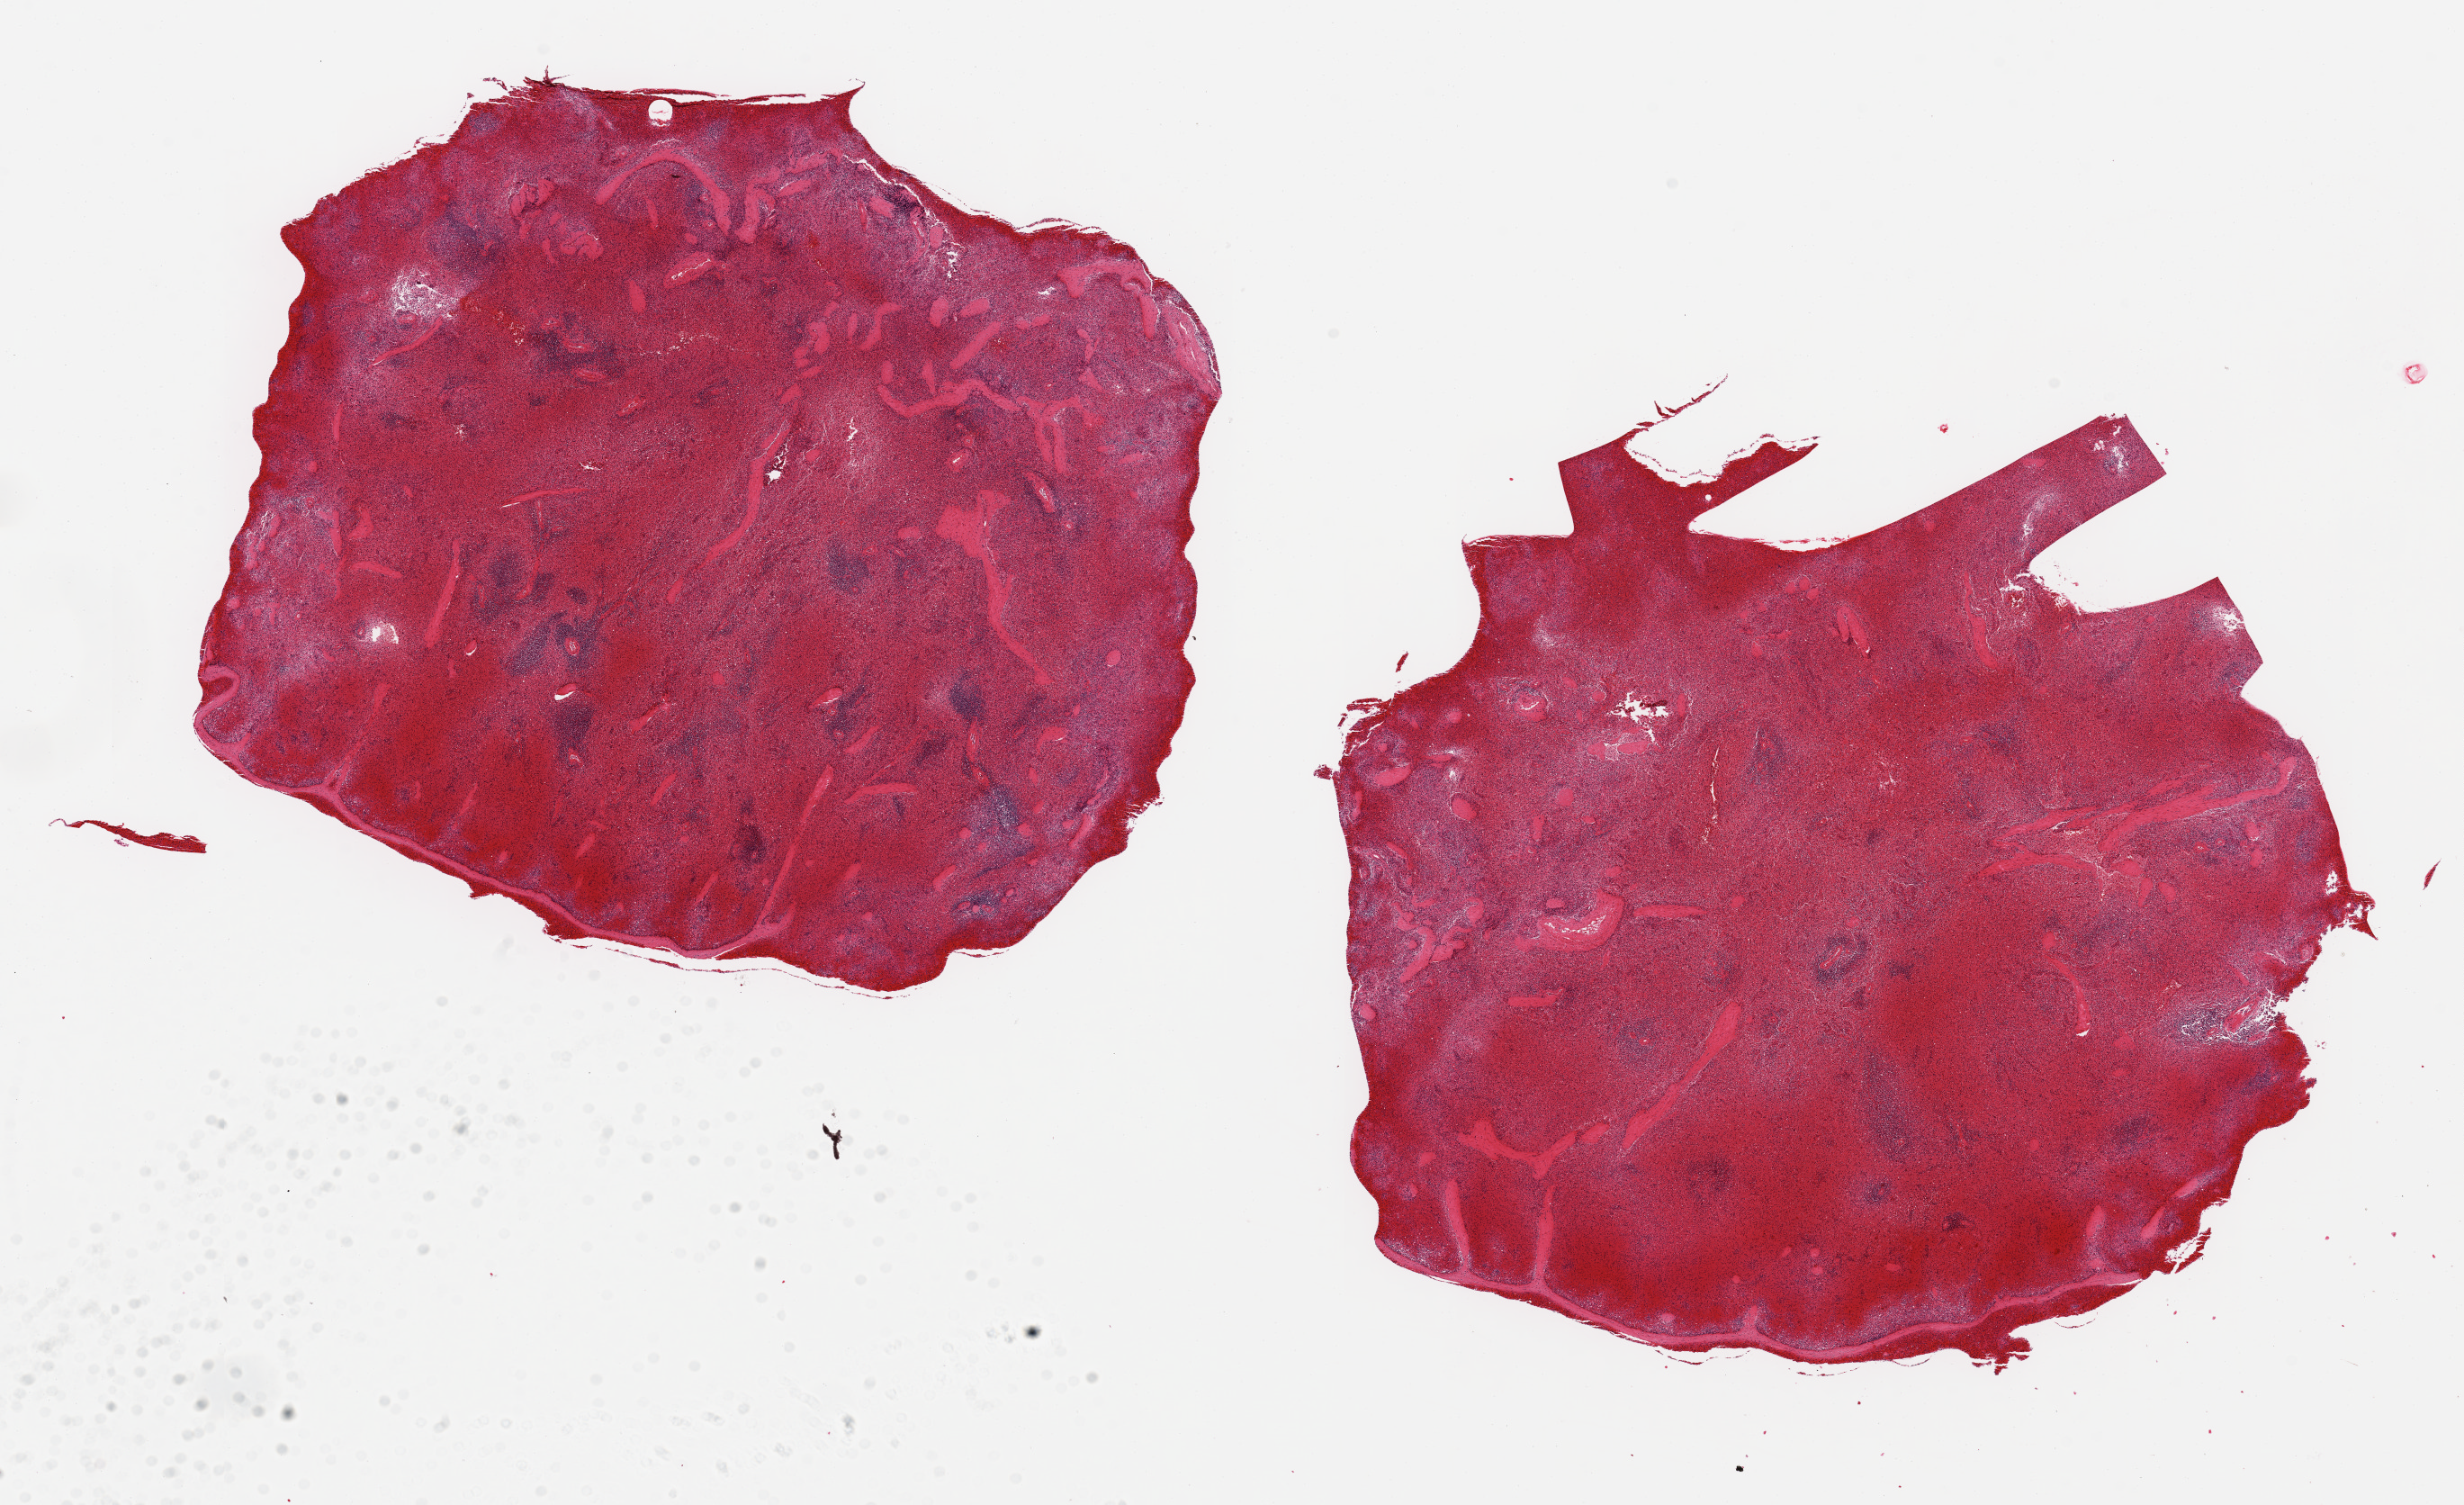
Digitized hematoxylin and eosin (H&E)-stained section, a low-resolution overview of the entire scanned area, about 21.7 x 13.2 mm (acquisition: 20x scan), PAXgene-fixed paraffin-embedded (PFPE) section, sampled site (target tissue): spleen, donor tissue sample. Female donor.
• review note (as recorded): 2 8x7.5mm aliquots. Appears under-fixed